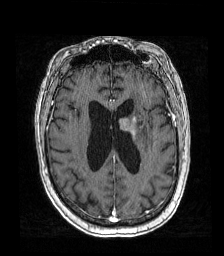
Brain MRI from a brain-tumour surgery series, one axial slice. Position 67 of 192 along the scan axis. T1-weighted post-contrast. 224 × 256 image matrix, field of view 219 × 250 mm. Case-level facts recorded for this patient, not image findings: histopathology: Metastatic carcinoma from lung primary; tumour location: Left Frontal Caudate.
Outlined on this slice (expert manual segmentation):
- tumour: box from (x=120, y=115) to (x=144, y=138) px